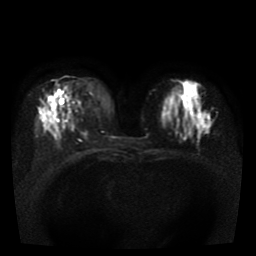
Breast MRI, one axial slice. Diffusion-weighted series; image 2 of 4 stored at this slice position (different b-values; order by instance number). 1.5 T. 256 × 256 image matrix, field of view 330 × 330 mm. Female patient.
Annotated regions visible in this slice (manually delineated by an expert):
- tumour on diffusion-weighted imaging: bounding box (x1, y1, x2, y2) in pixels: (195, 110, 212, 130)